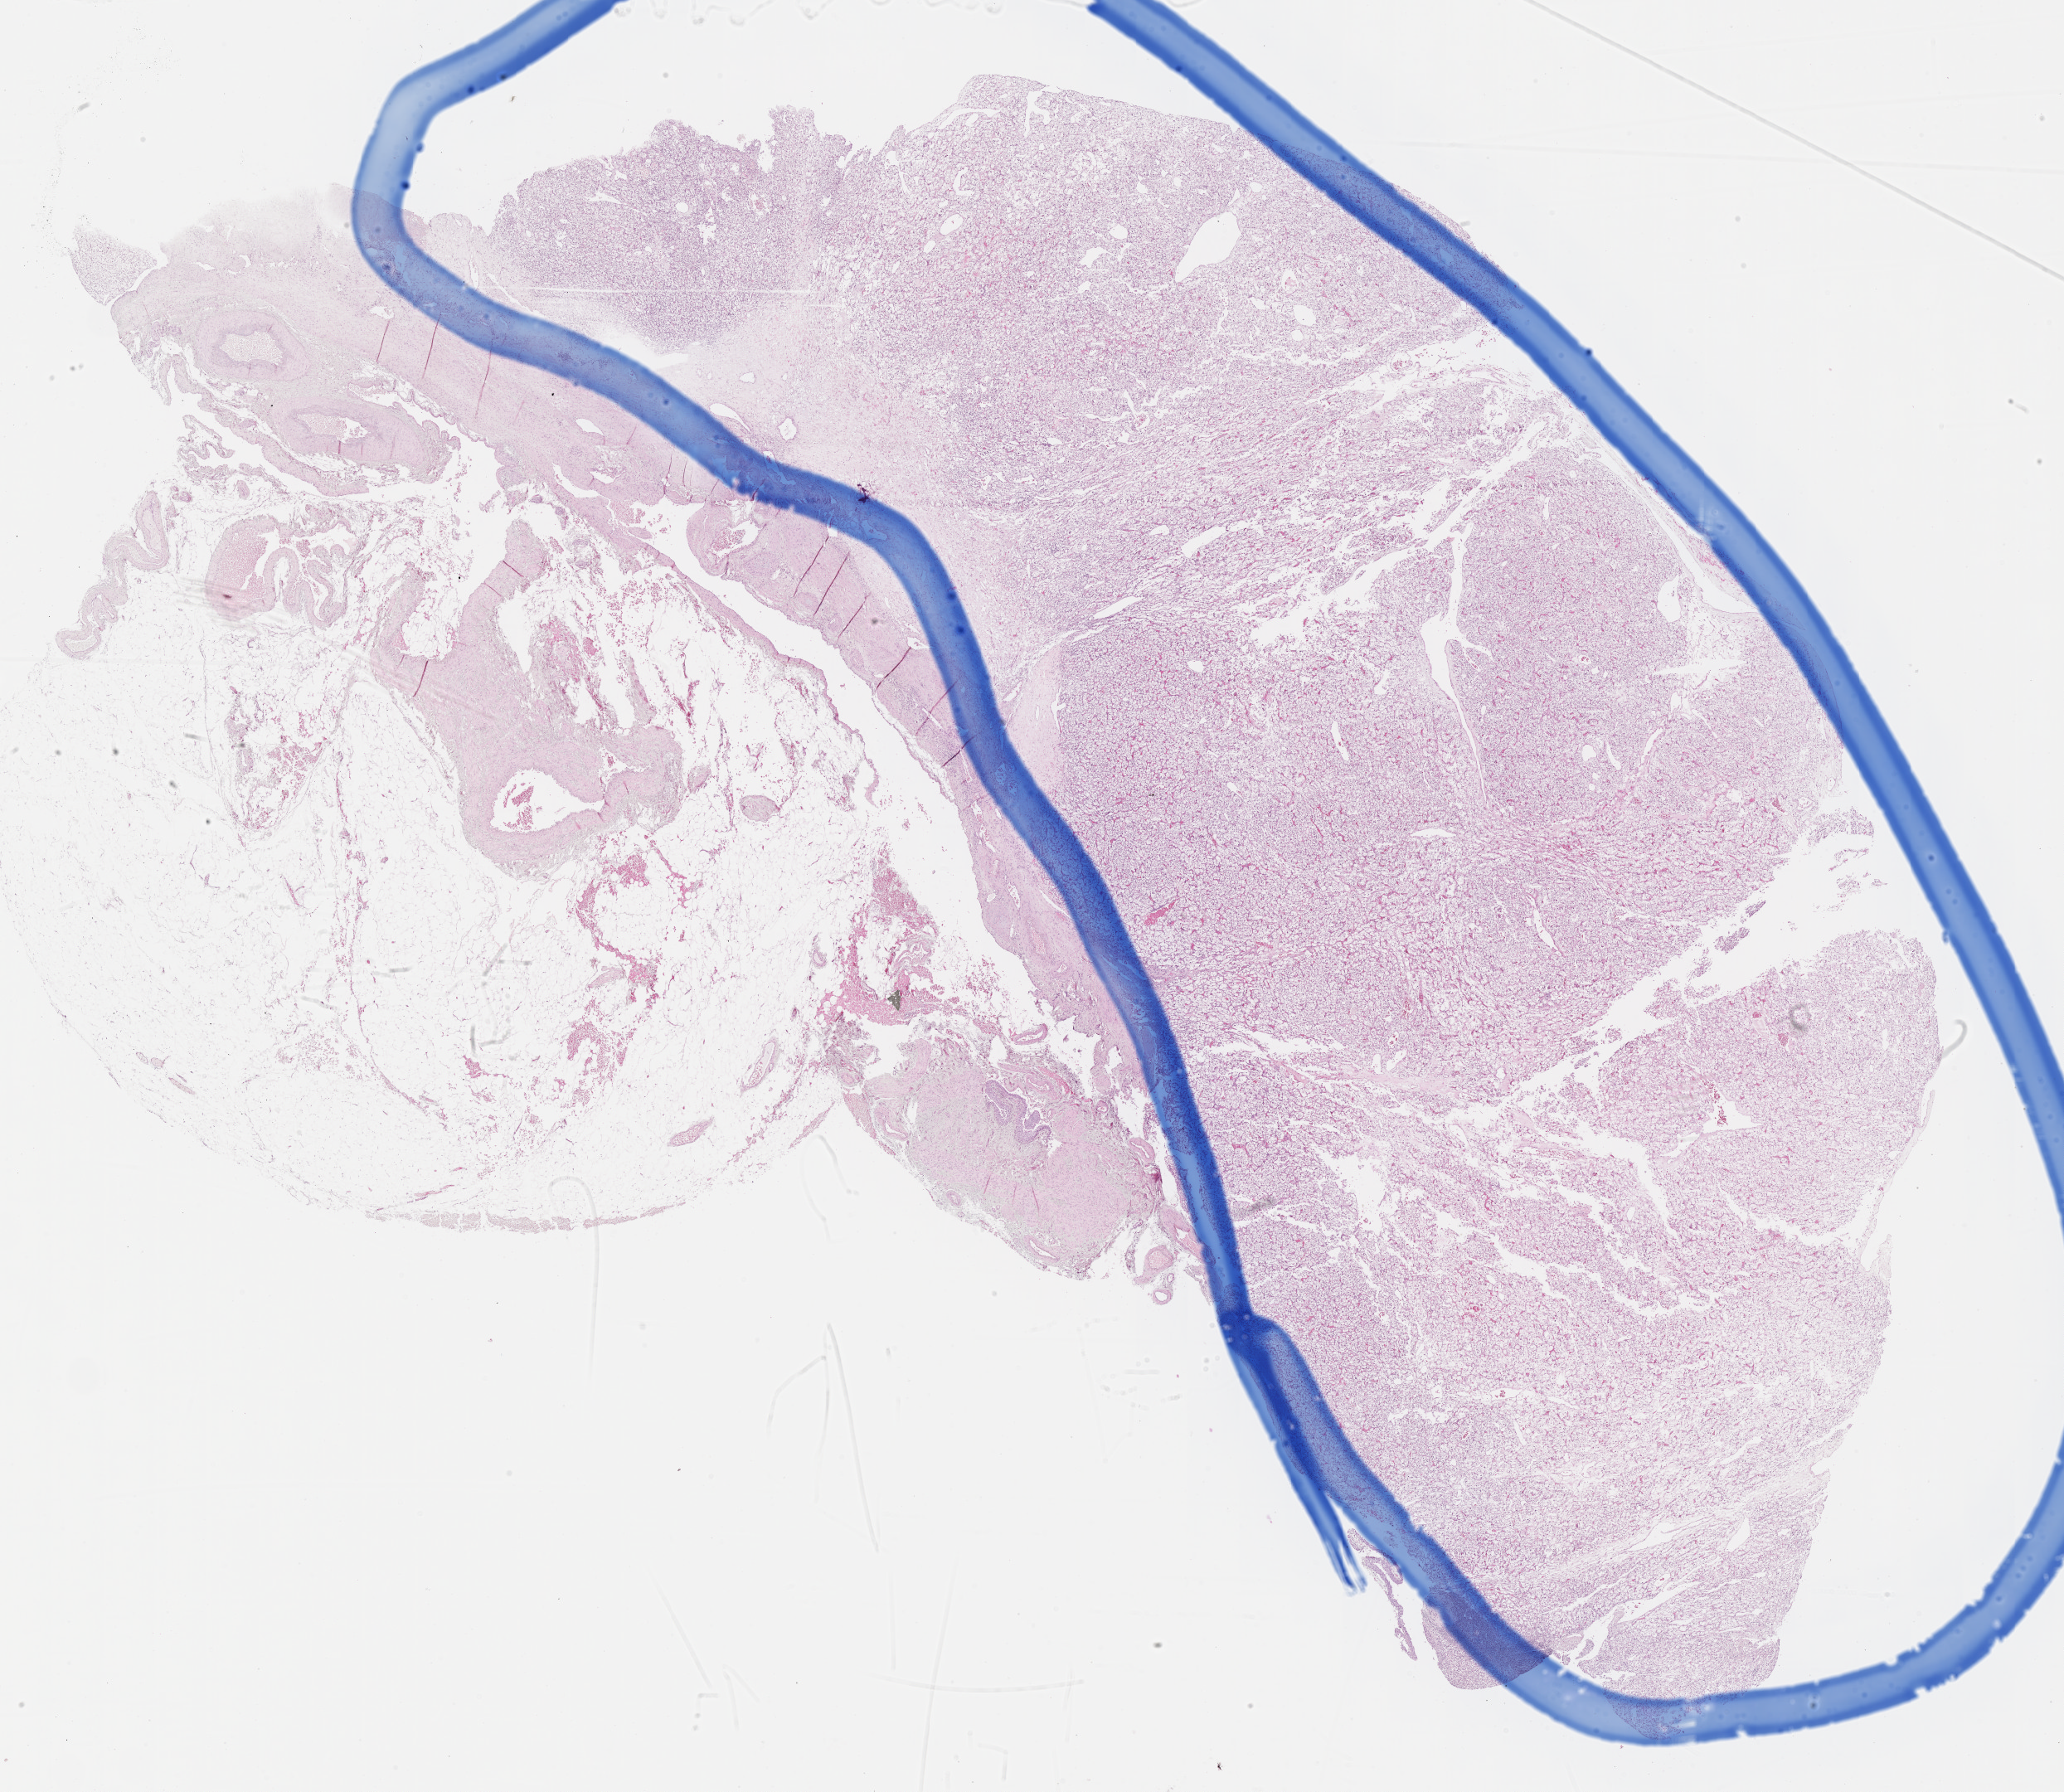
H&E whole-slide image — a low-resolution overview of the entire scanned area, about 20.1 x 17.5 mm (slide scanned at 40x). FFPE section. Sample: primary tumour, kidney. Female, age 76 years at initial diagnosis.
Diagnosis: Clear cell adenocarcinoma, NOS.